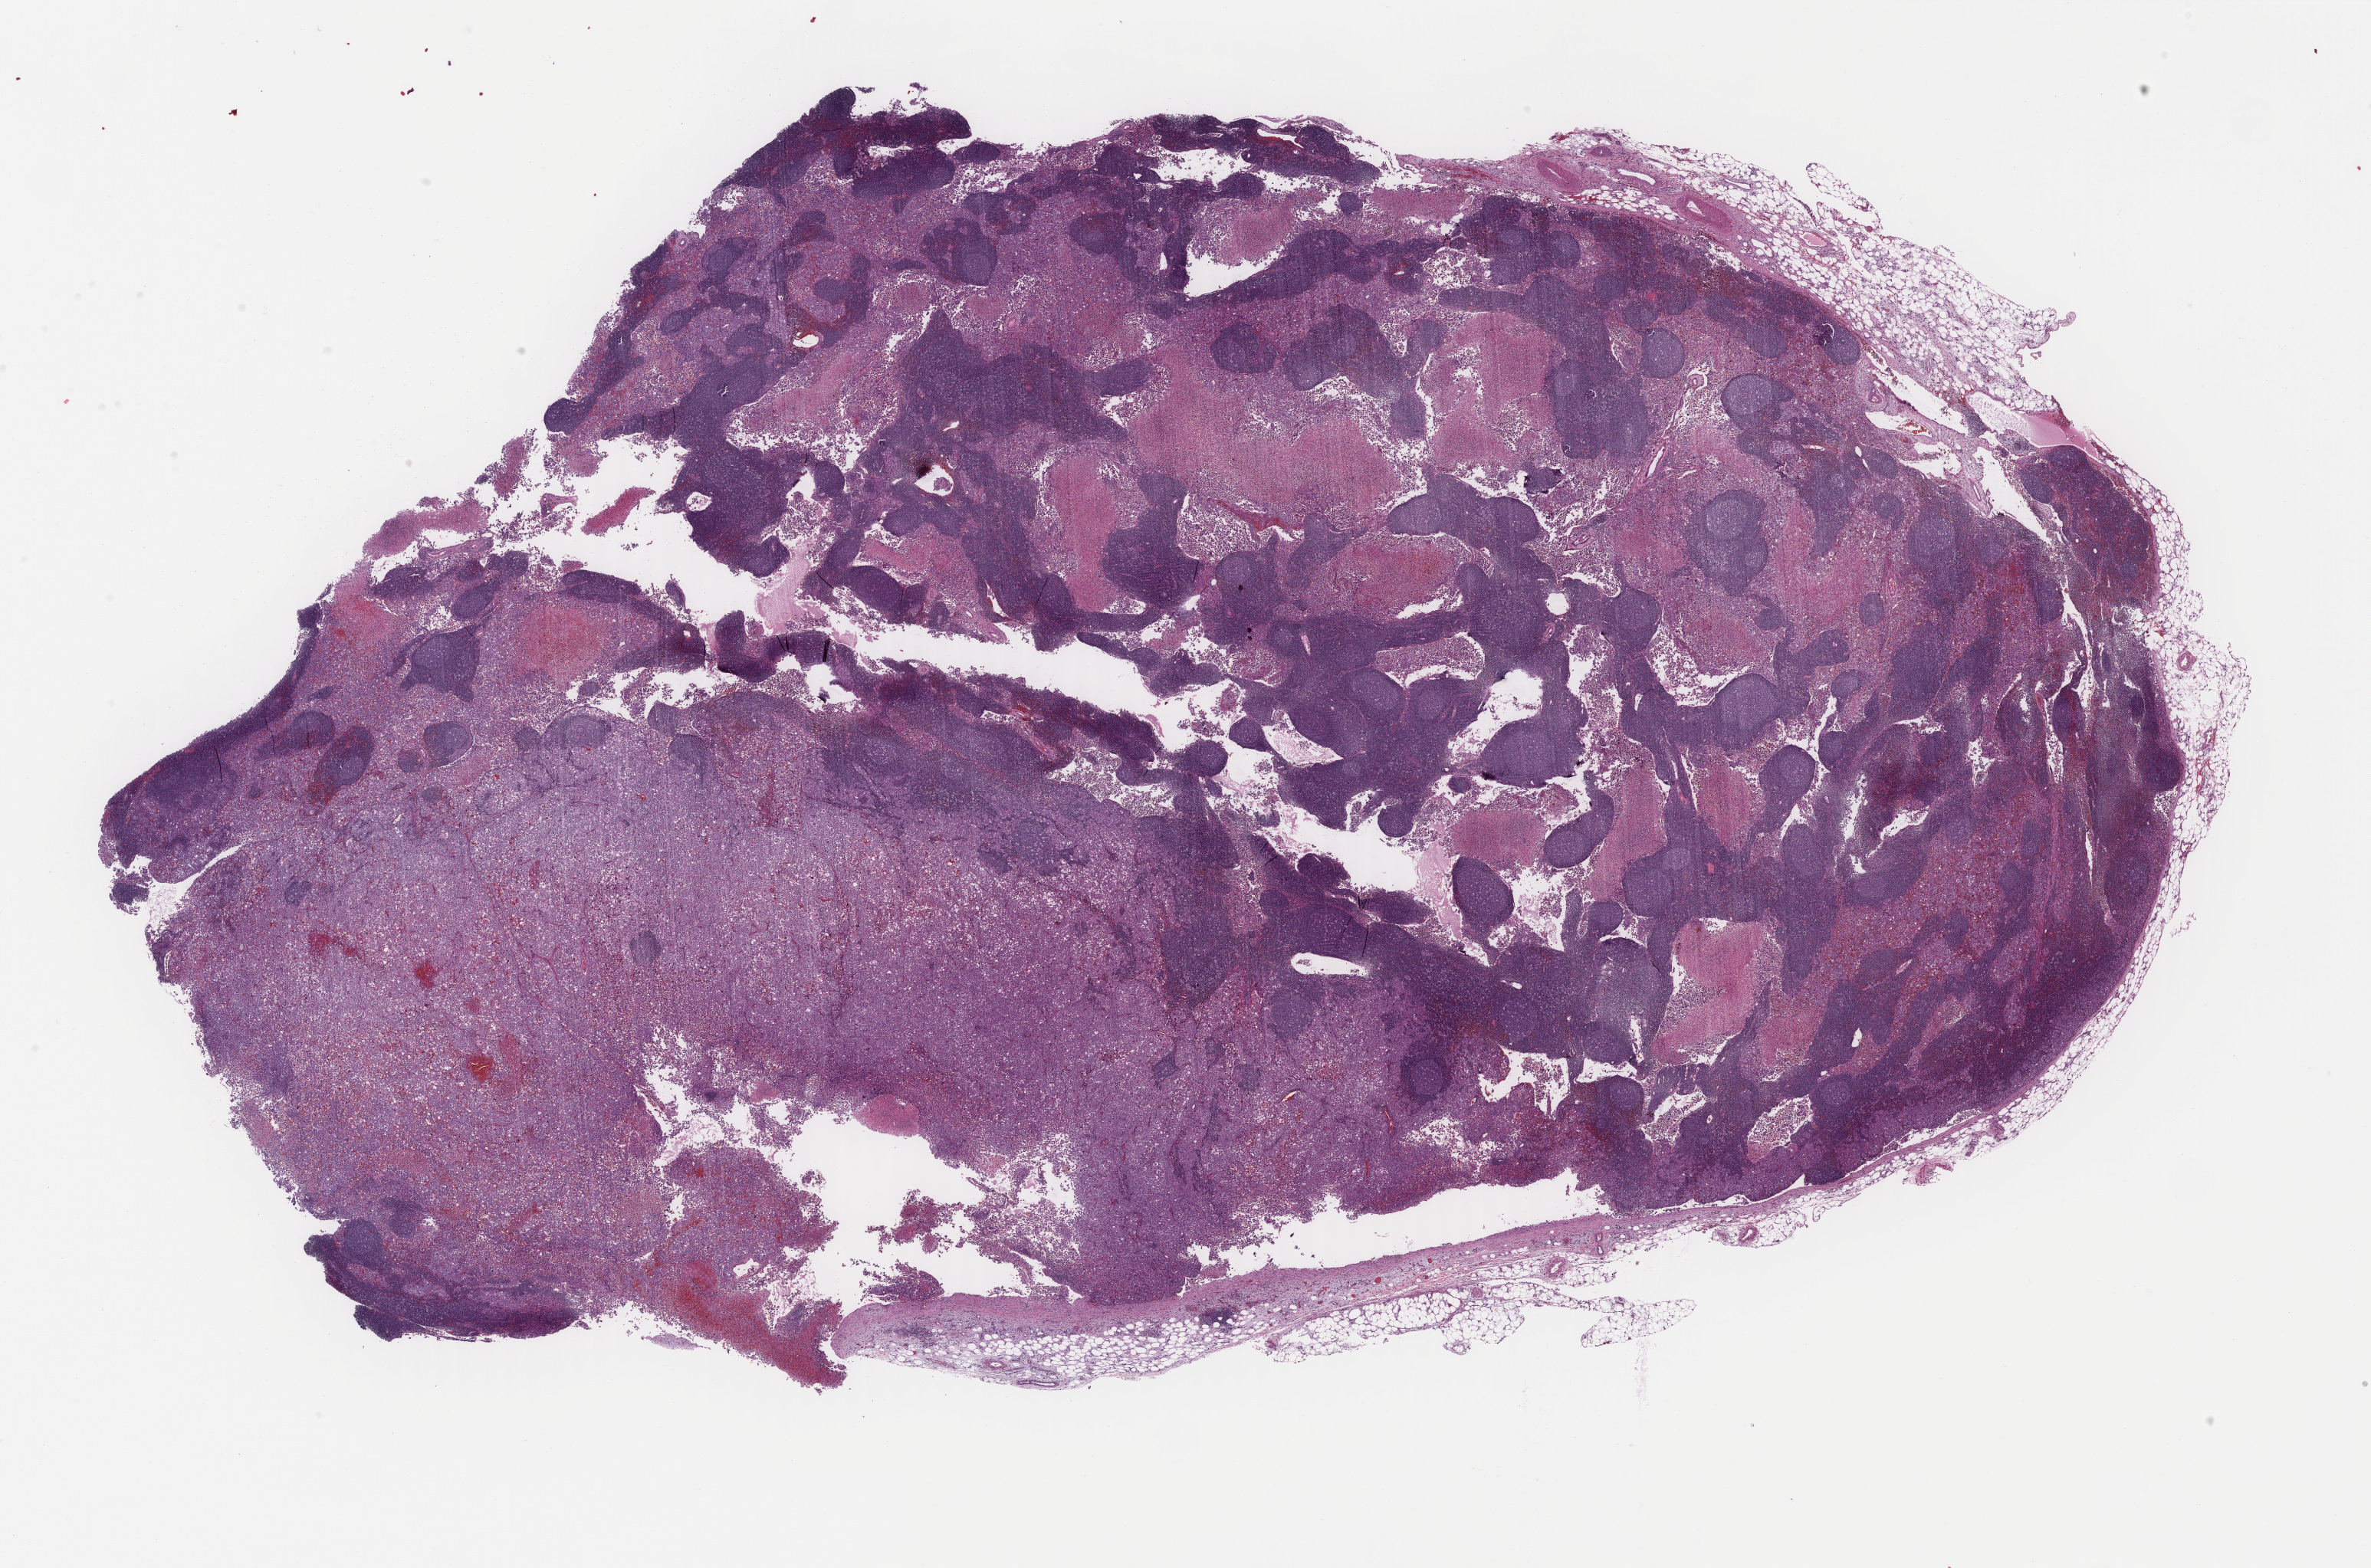
Whole-slide histology image, H&E-stained, low-resolution overview of the scanned area, about 24.6 x 16.2 mm (from a 40x scan). Formalin-fixed paraffin-embedded (FFPE) diagnostic section. Metastatic tumour sample, sampled site: skin of scalp and neck. Male patient; age at initial diagnosis 58 years.
* this section: metastatic tumour tissue
* patient diagnosis: Malignant melanoma, NOS